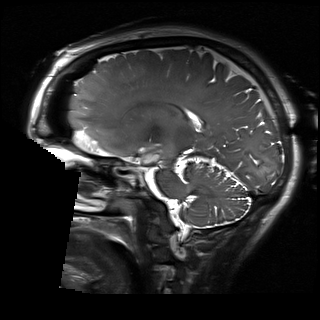
Brain MRI from a brain-tumour surgery series, one sagittal slice. Slice 111 of 192 in the series (ordered by position). 1 mm slice thickness. 320 × 320 image matrix, field of view 230 × 230 mm. From the clinical record (not read from this slice): histopathology: Glioblastoma; WHO grade: 2; IDH mutation: no.
Structures marked on this image (manually delineated by an expert):
- residual tumour: bounding box <144,153,159,163> (left, top, right, bottom; pixels)